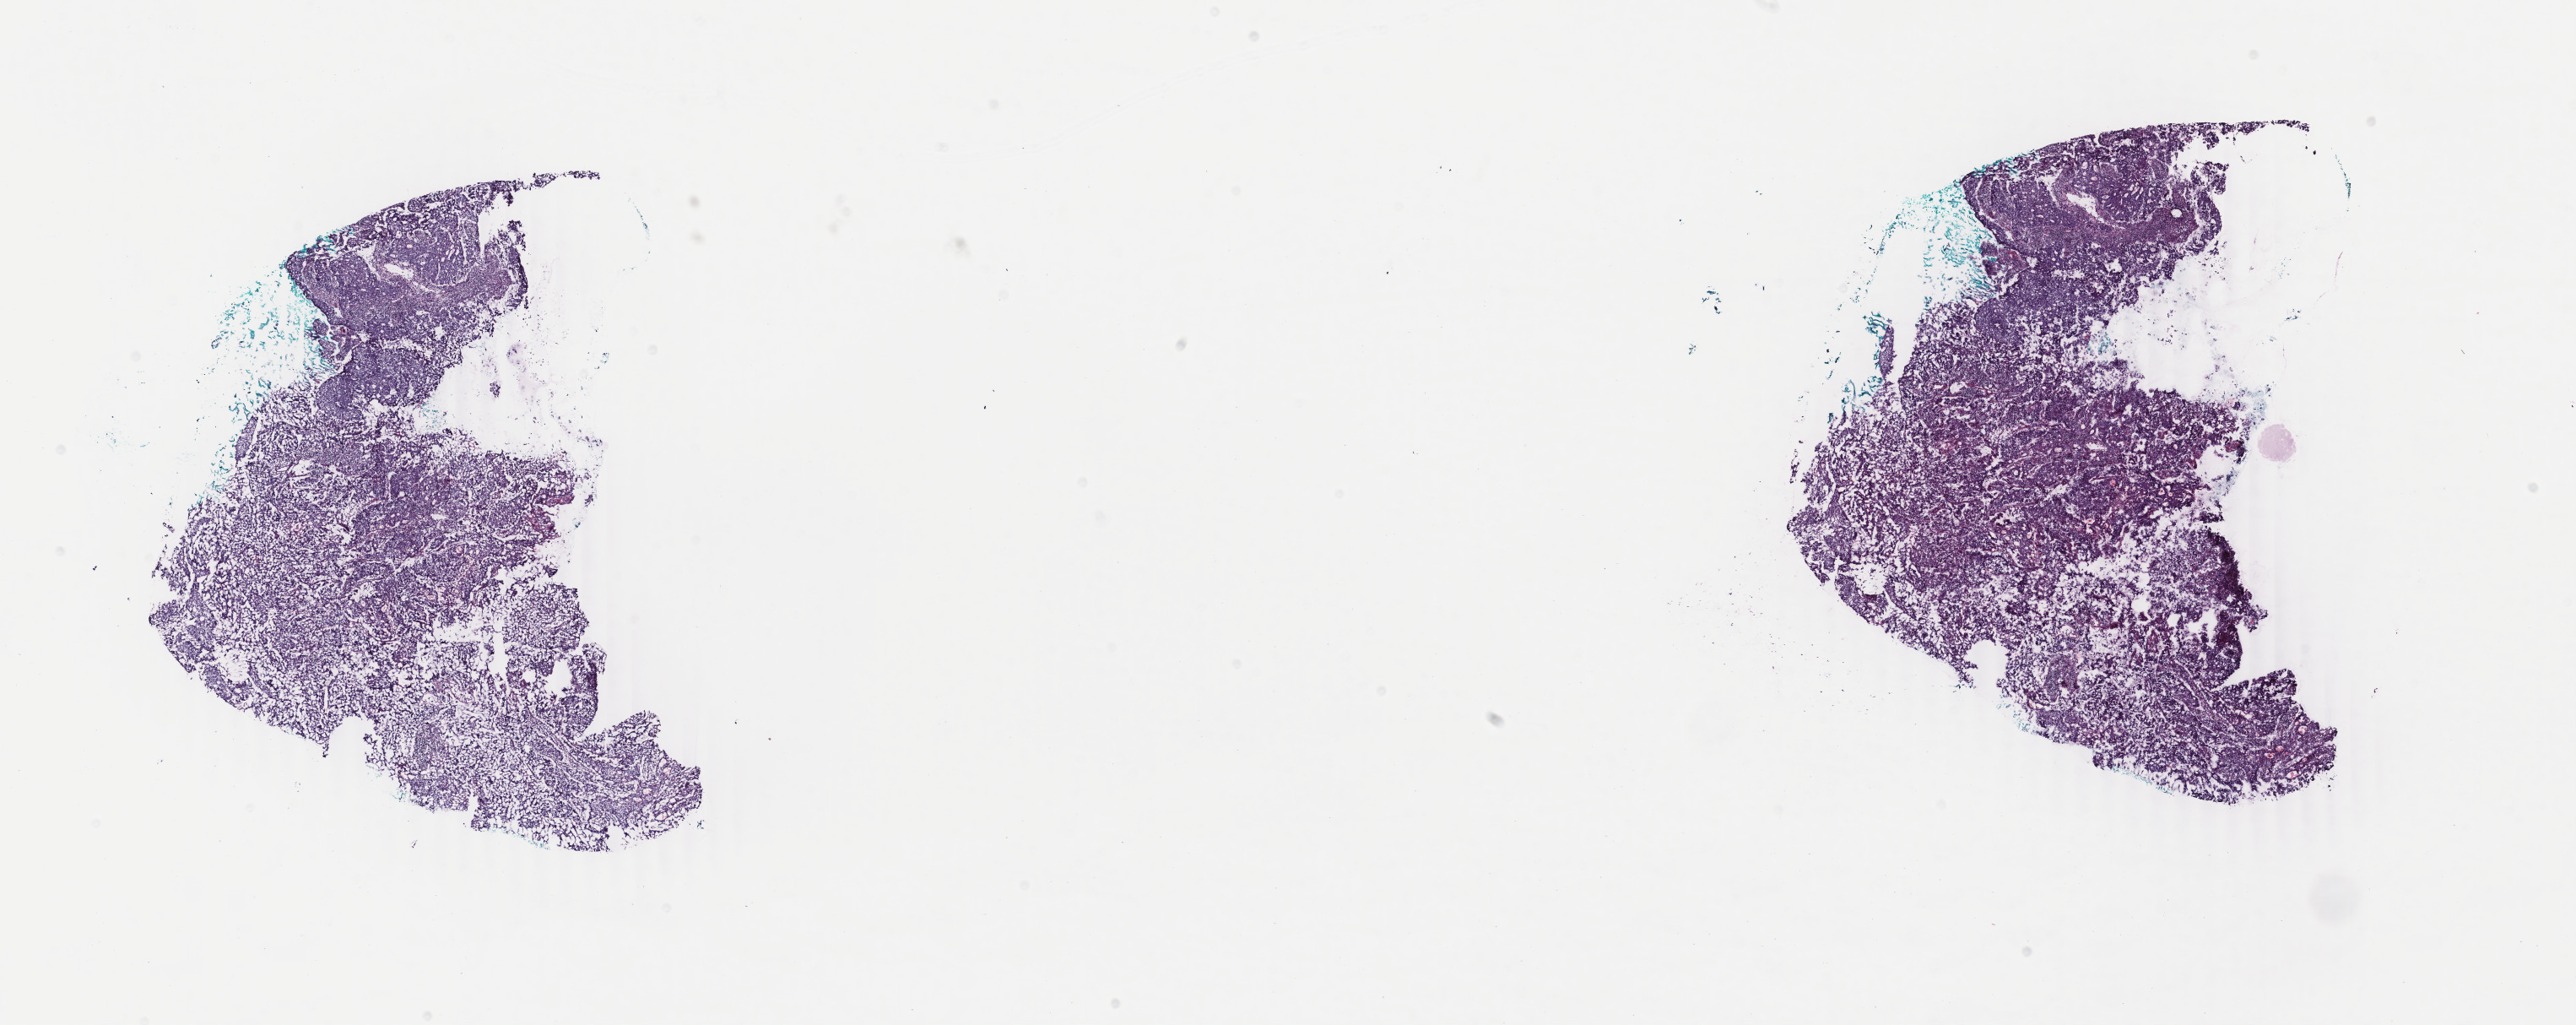
Whole-slide histology image, H&E — a low-resolution overview of the entire scanned area, about 24.3 x 9.7 mm (acquisition: 40x scan). Frozen section from the bottom of the tissue portion. Primary tumour sample from the uterus. Female patient; age at initial diagnosis 35 years. Slide review estimates, as recorded: tumour cells 85%, tumour nuclei 85%.
Pathologic diagnosis: Endometrioid adenocarcinoma, NOS (corpus uteri).